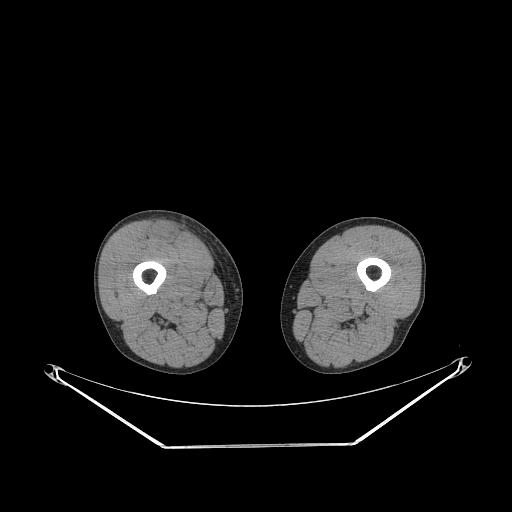
CT of an extremity soft-tissue mass (from a PET/CT study), one axial slice. 140 kVp. Soft-tissue window (W 400 / L 40 HU). 3.75 mm slice thickness. 512 × 512 image matrix. Male patient. Case-level facts recorded for this patient, not image findings: histological type: pleiomorphic leiomyosarcoma; grade: intermediate; site of the primary tumour: right thigh.
Outlined on this slice (expert contour drawn on MRI and transferred to this co-registered scan by the dataset authors):
- gross tumour volume including surrounding oedema: box from (x=153, y=224) to (x=181, y=243) px